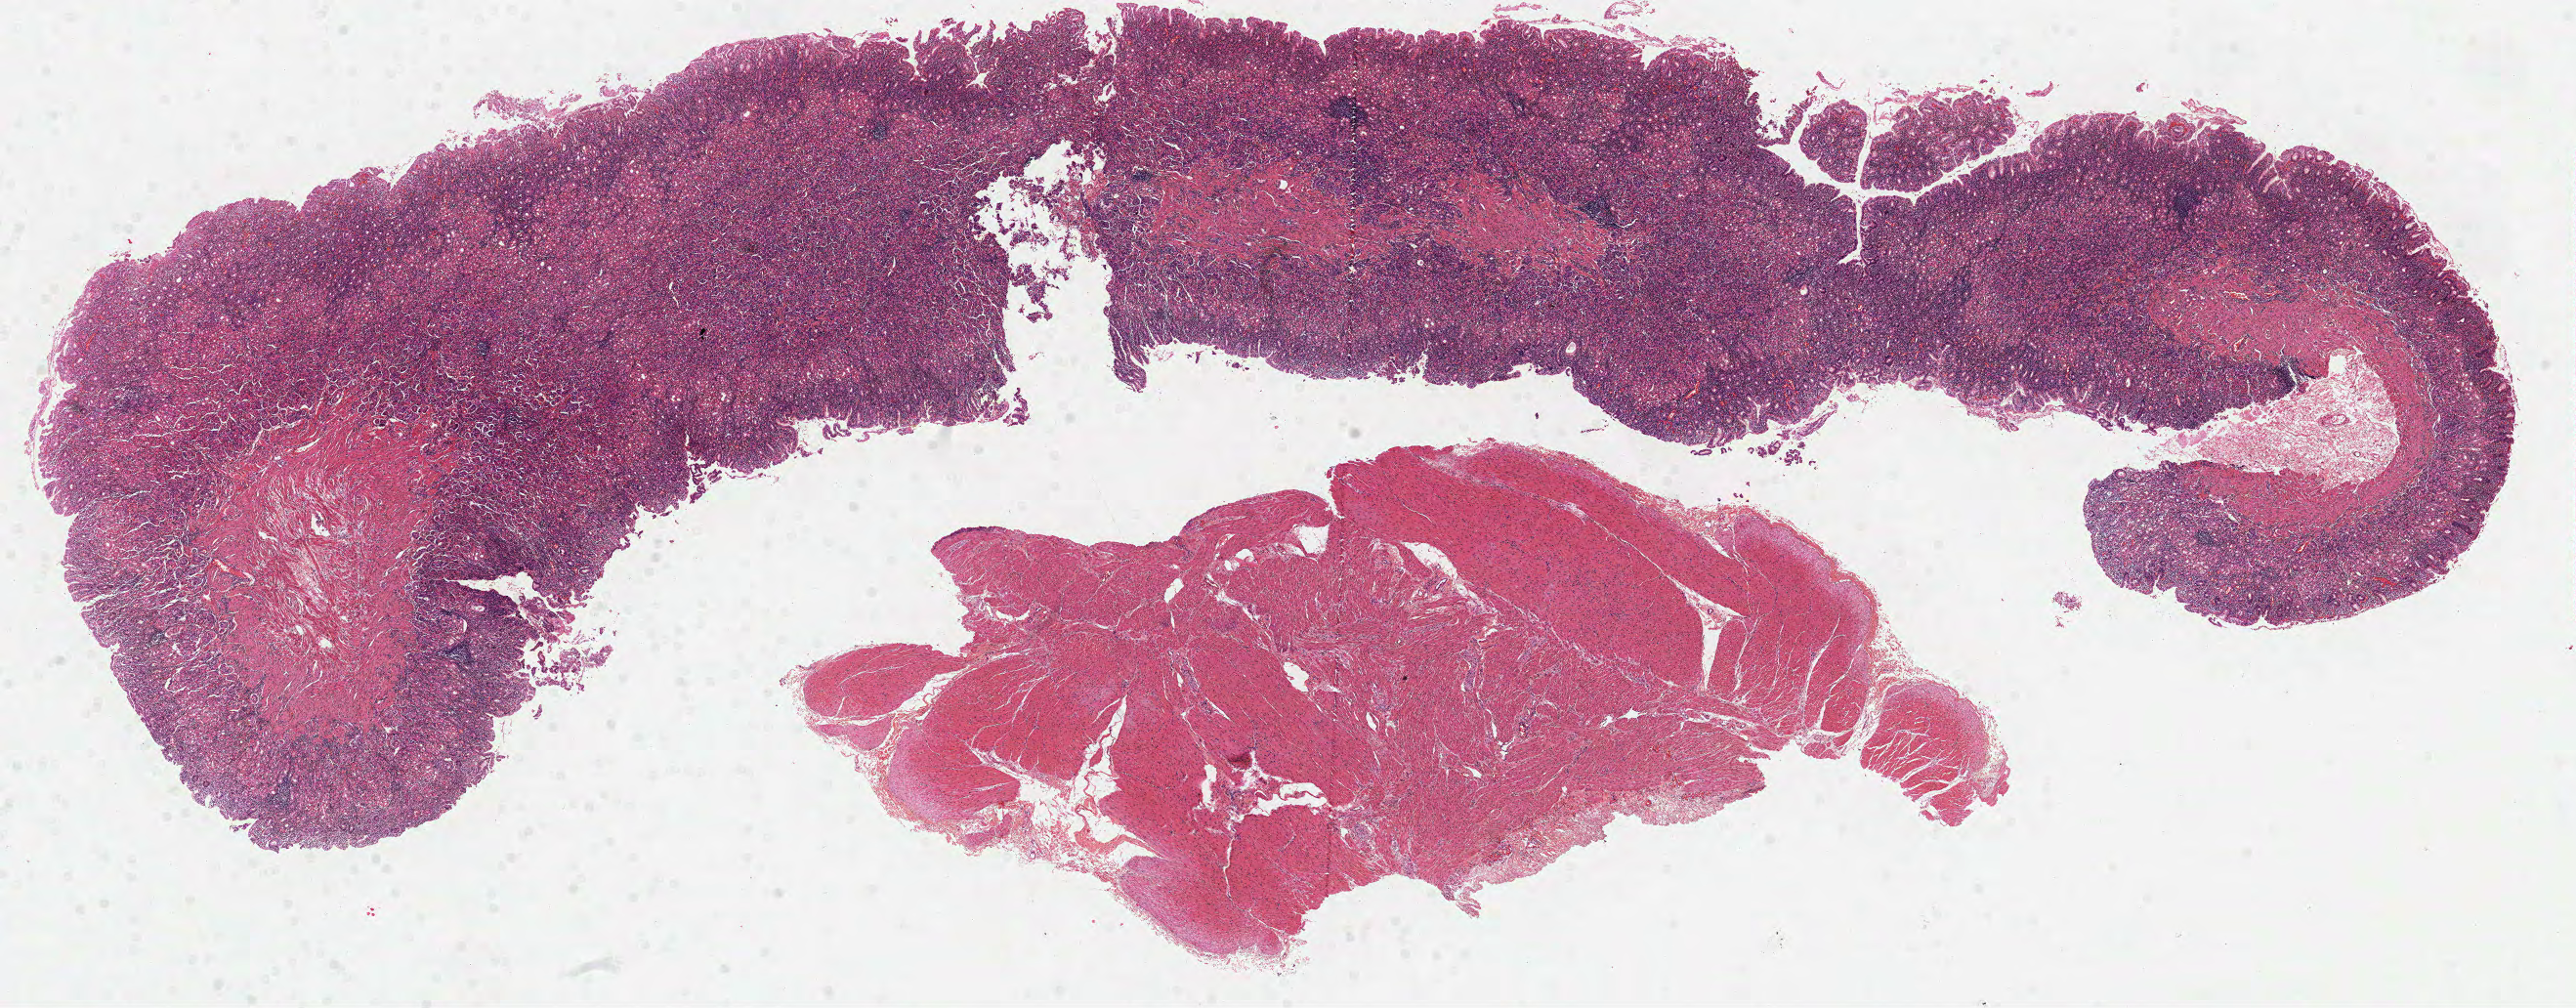
Whole-slide histology image, Hematoxylin and eosin (H&E) stained, low-resolution overview of the scanned area, about 21.3 x 8.3 mm, formalin-fixed paraffin-embedded (FFPE) diagnostic section, sample: primary tumour, stomach. Female patient; age at initial diagnosis 51 years. Histologic grade: G3 (poorly differentiated).
Lymph nodes positive (case pathology): 0 of 9 examined. Diagnosis: Carcinoma, diffuse type. AJCC pathologic stage: IIB (7th edition).